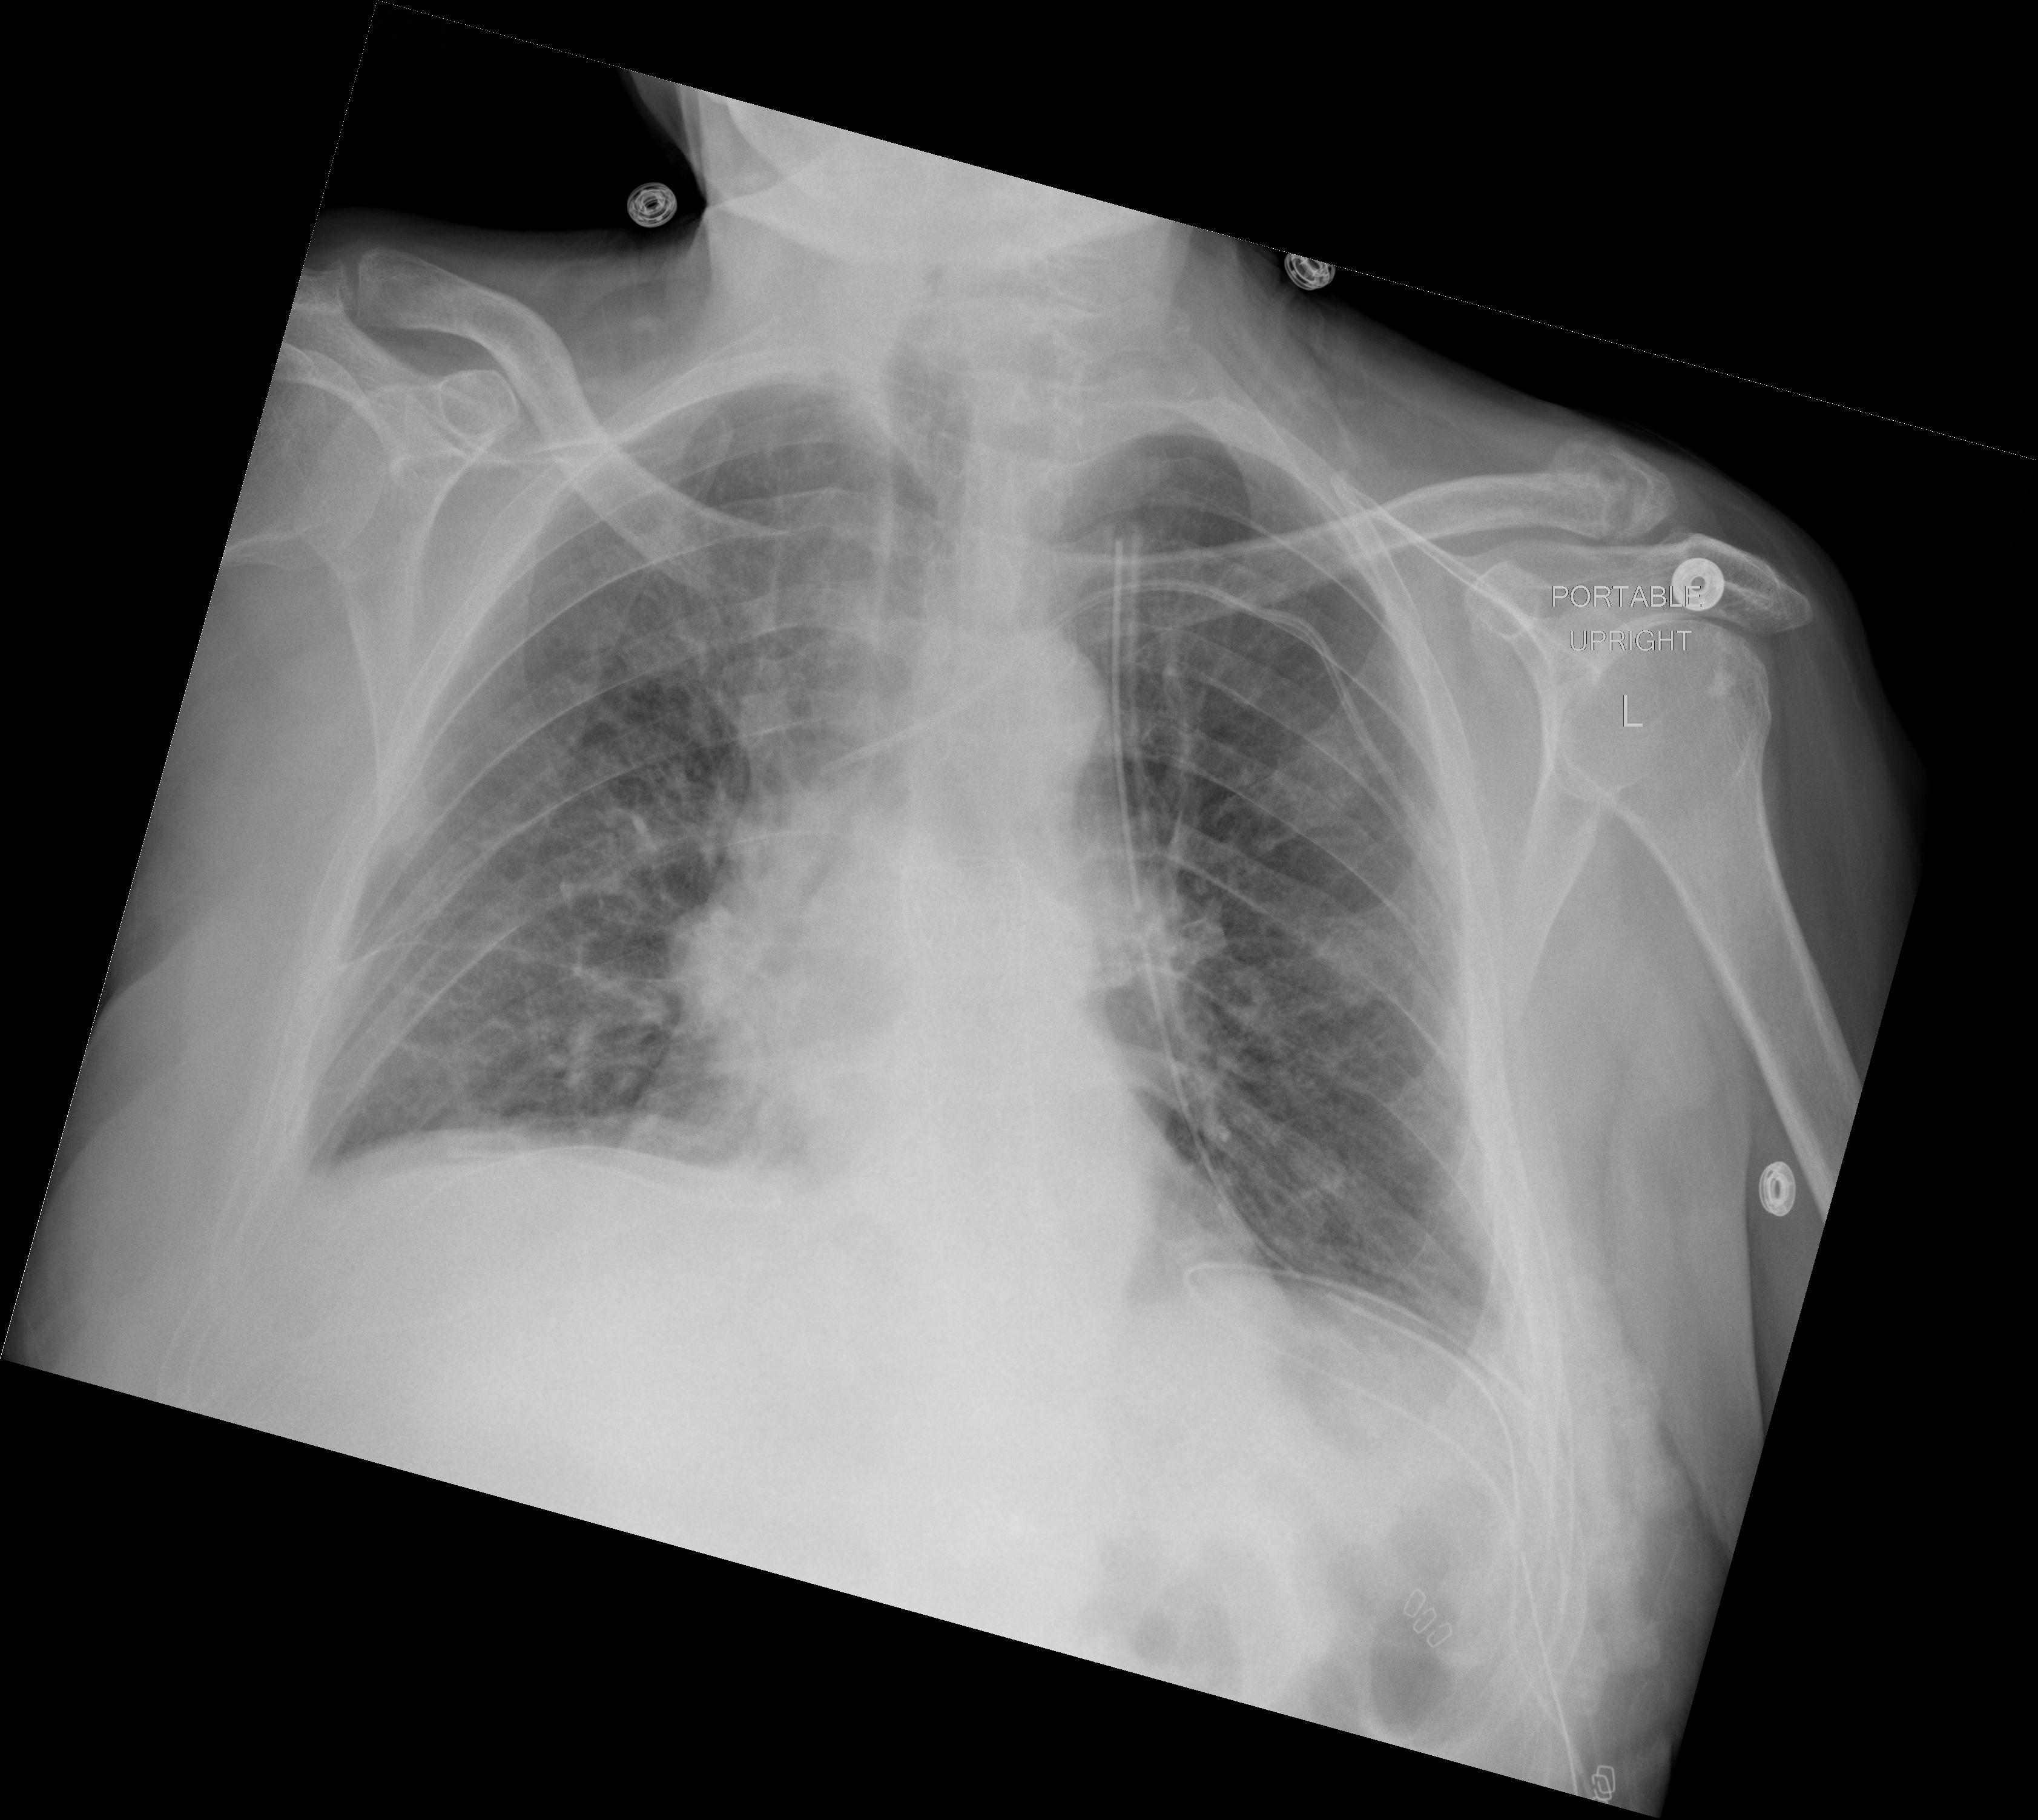
Chest X-ray (portable), AP projection. Male patient, age 64 years; imaged 9 days after the COVID-19 diagnosis.
Key findings recorded by the radiologist: Persistent linear atelectasis is seen within the bilateral lung bases. Probable small bilateral pleural effusions.